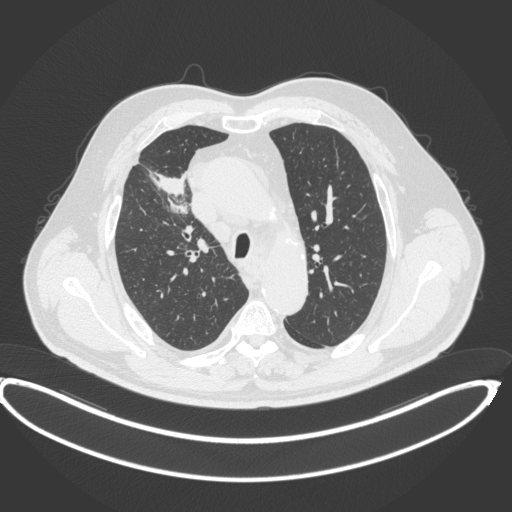
Chest CT, one axial slice. Position 295 of 395 along the scan axis. Reconstruction kernel B31f. 120 kVp. Lung window (W 1500 / L -600 HU). 512 × 512 image matrix. Patient: male, 62 years. From the clinical record (not read from this slice): clinical TNM (as recorded): T1c N3 M1c.
Structures marked on this image (bounding box drawn by a radiologist):
- lung tumour (recorded histology: adenocarcinoma): bounding box (x1, y1, x2, y2) in pixels: (148, 168, 191, 218)